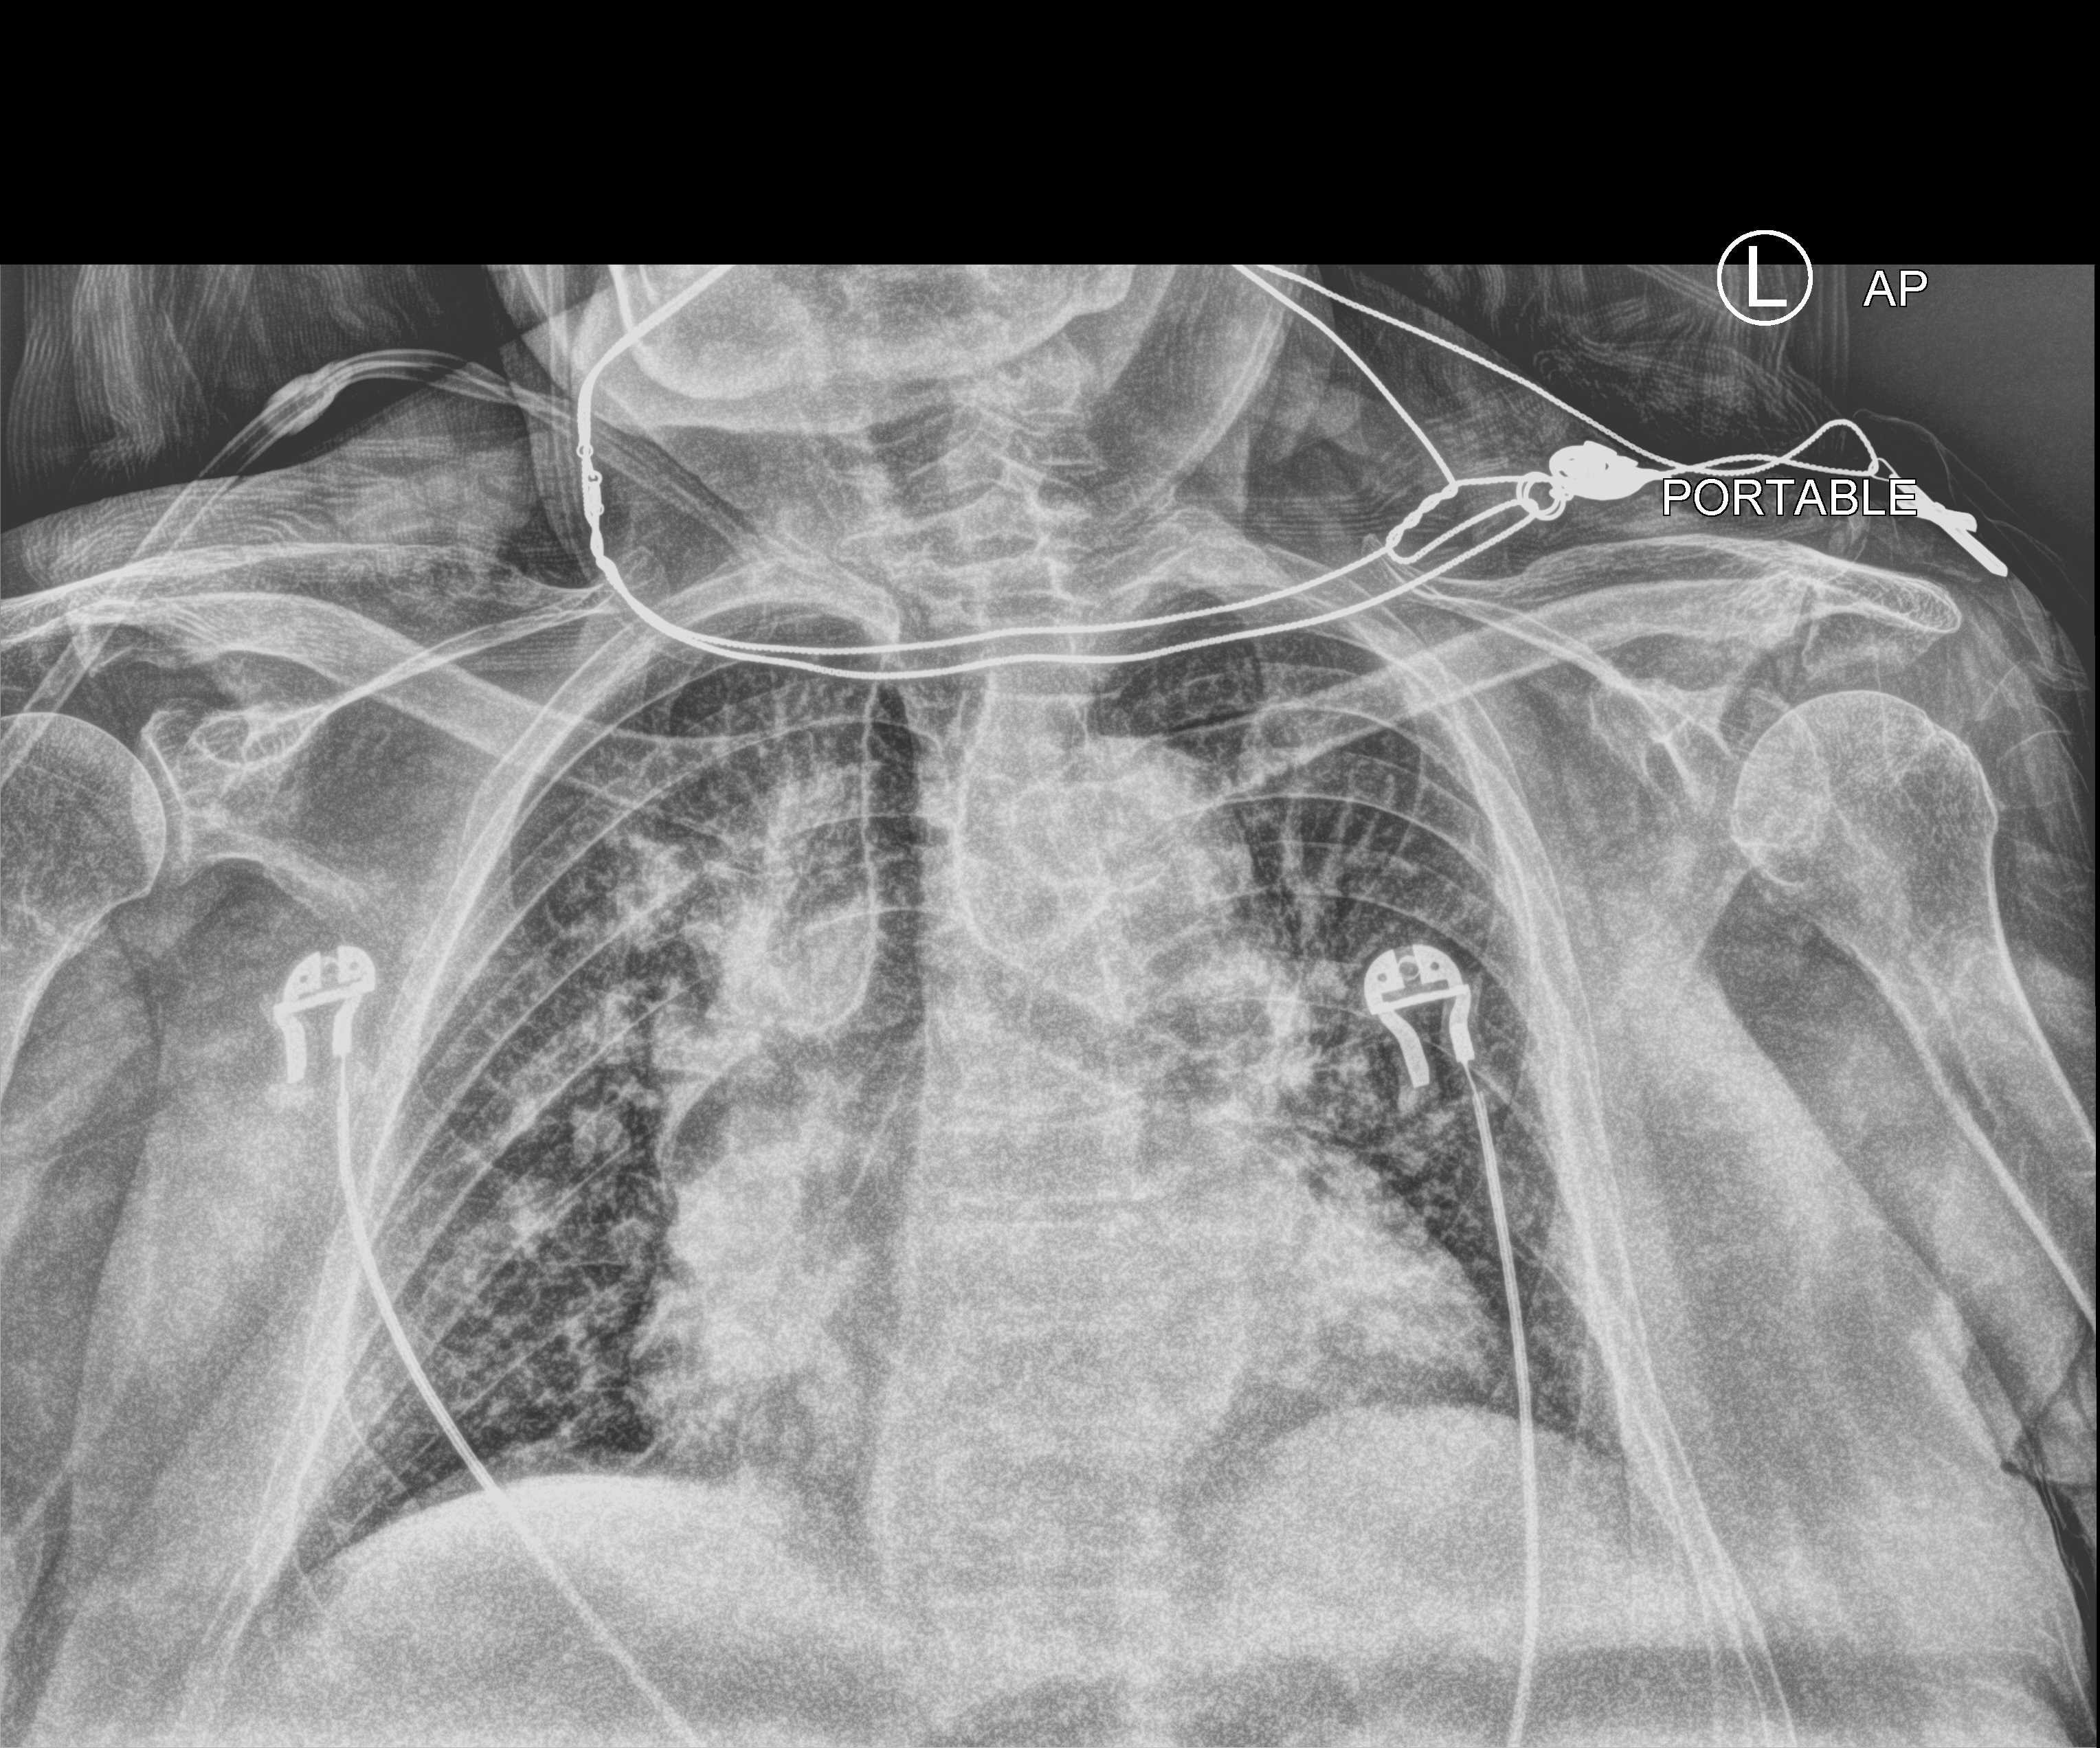
Chest X-ray (portable), anteroposterior (AP) projection. Patient hospitalised with COVID-19; female, aged 75–90 years.
From the hospital-stay record, not from the radiograph (when in the stay this image was taken is not recorded): mechanically ventilated during this hospital stay: no.